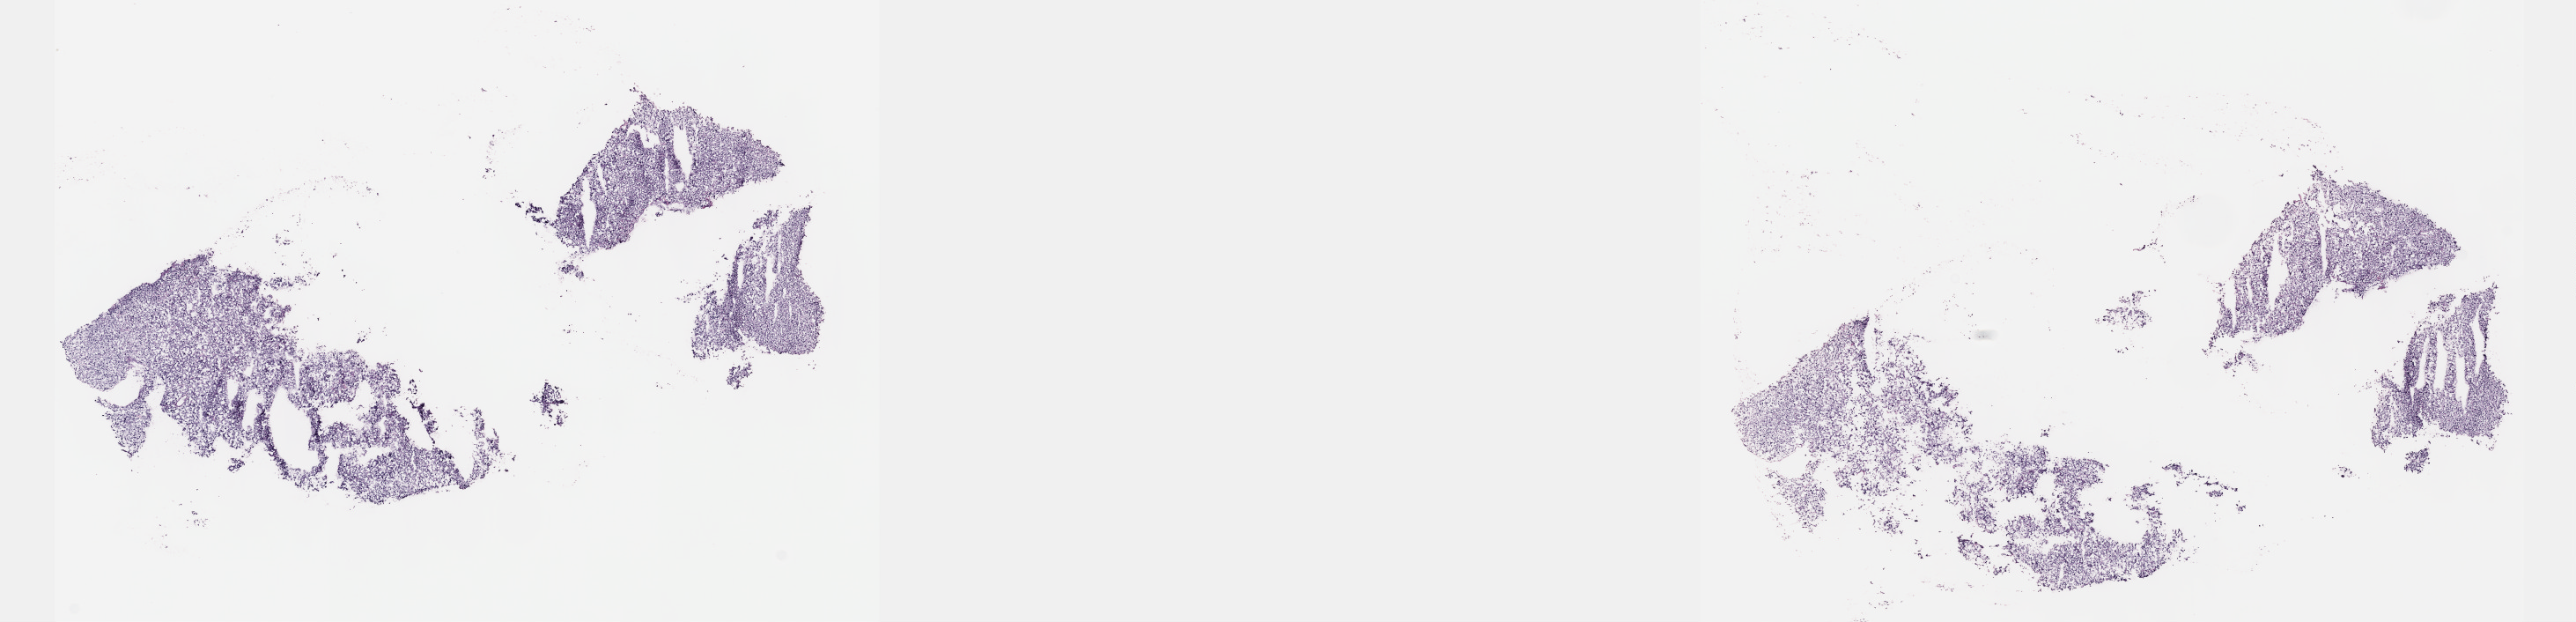
H&E whole-slide image — whole scanned area (about 23.6 x 5.7 mm, slide scanned at 40x) shown as a low-resolution overview; frozen section from the top of the tissue portion; primary tumour sample from the retroperitoneum and peritoneum. Patient: female, age at initial diagnosis 75 years.
Diagnosis: Extra-adrenal paraganglioma, NOS (retroperitoneum).